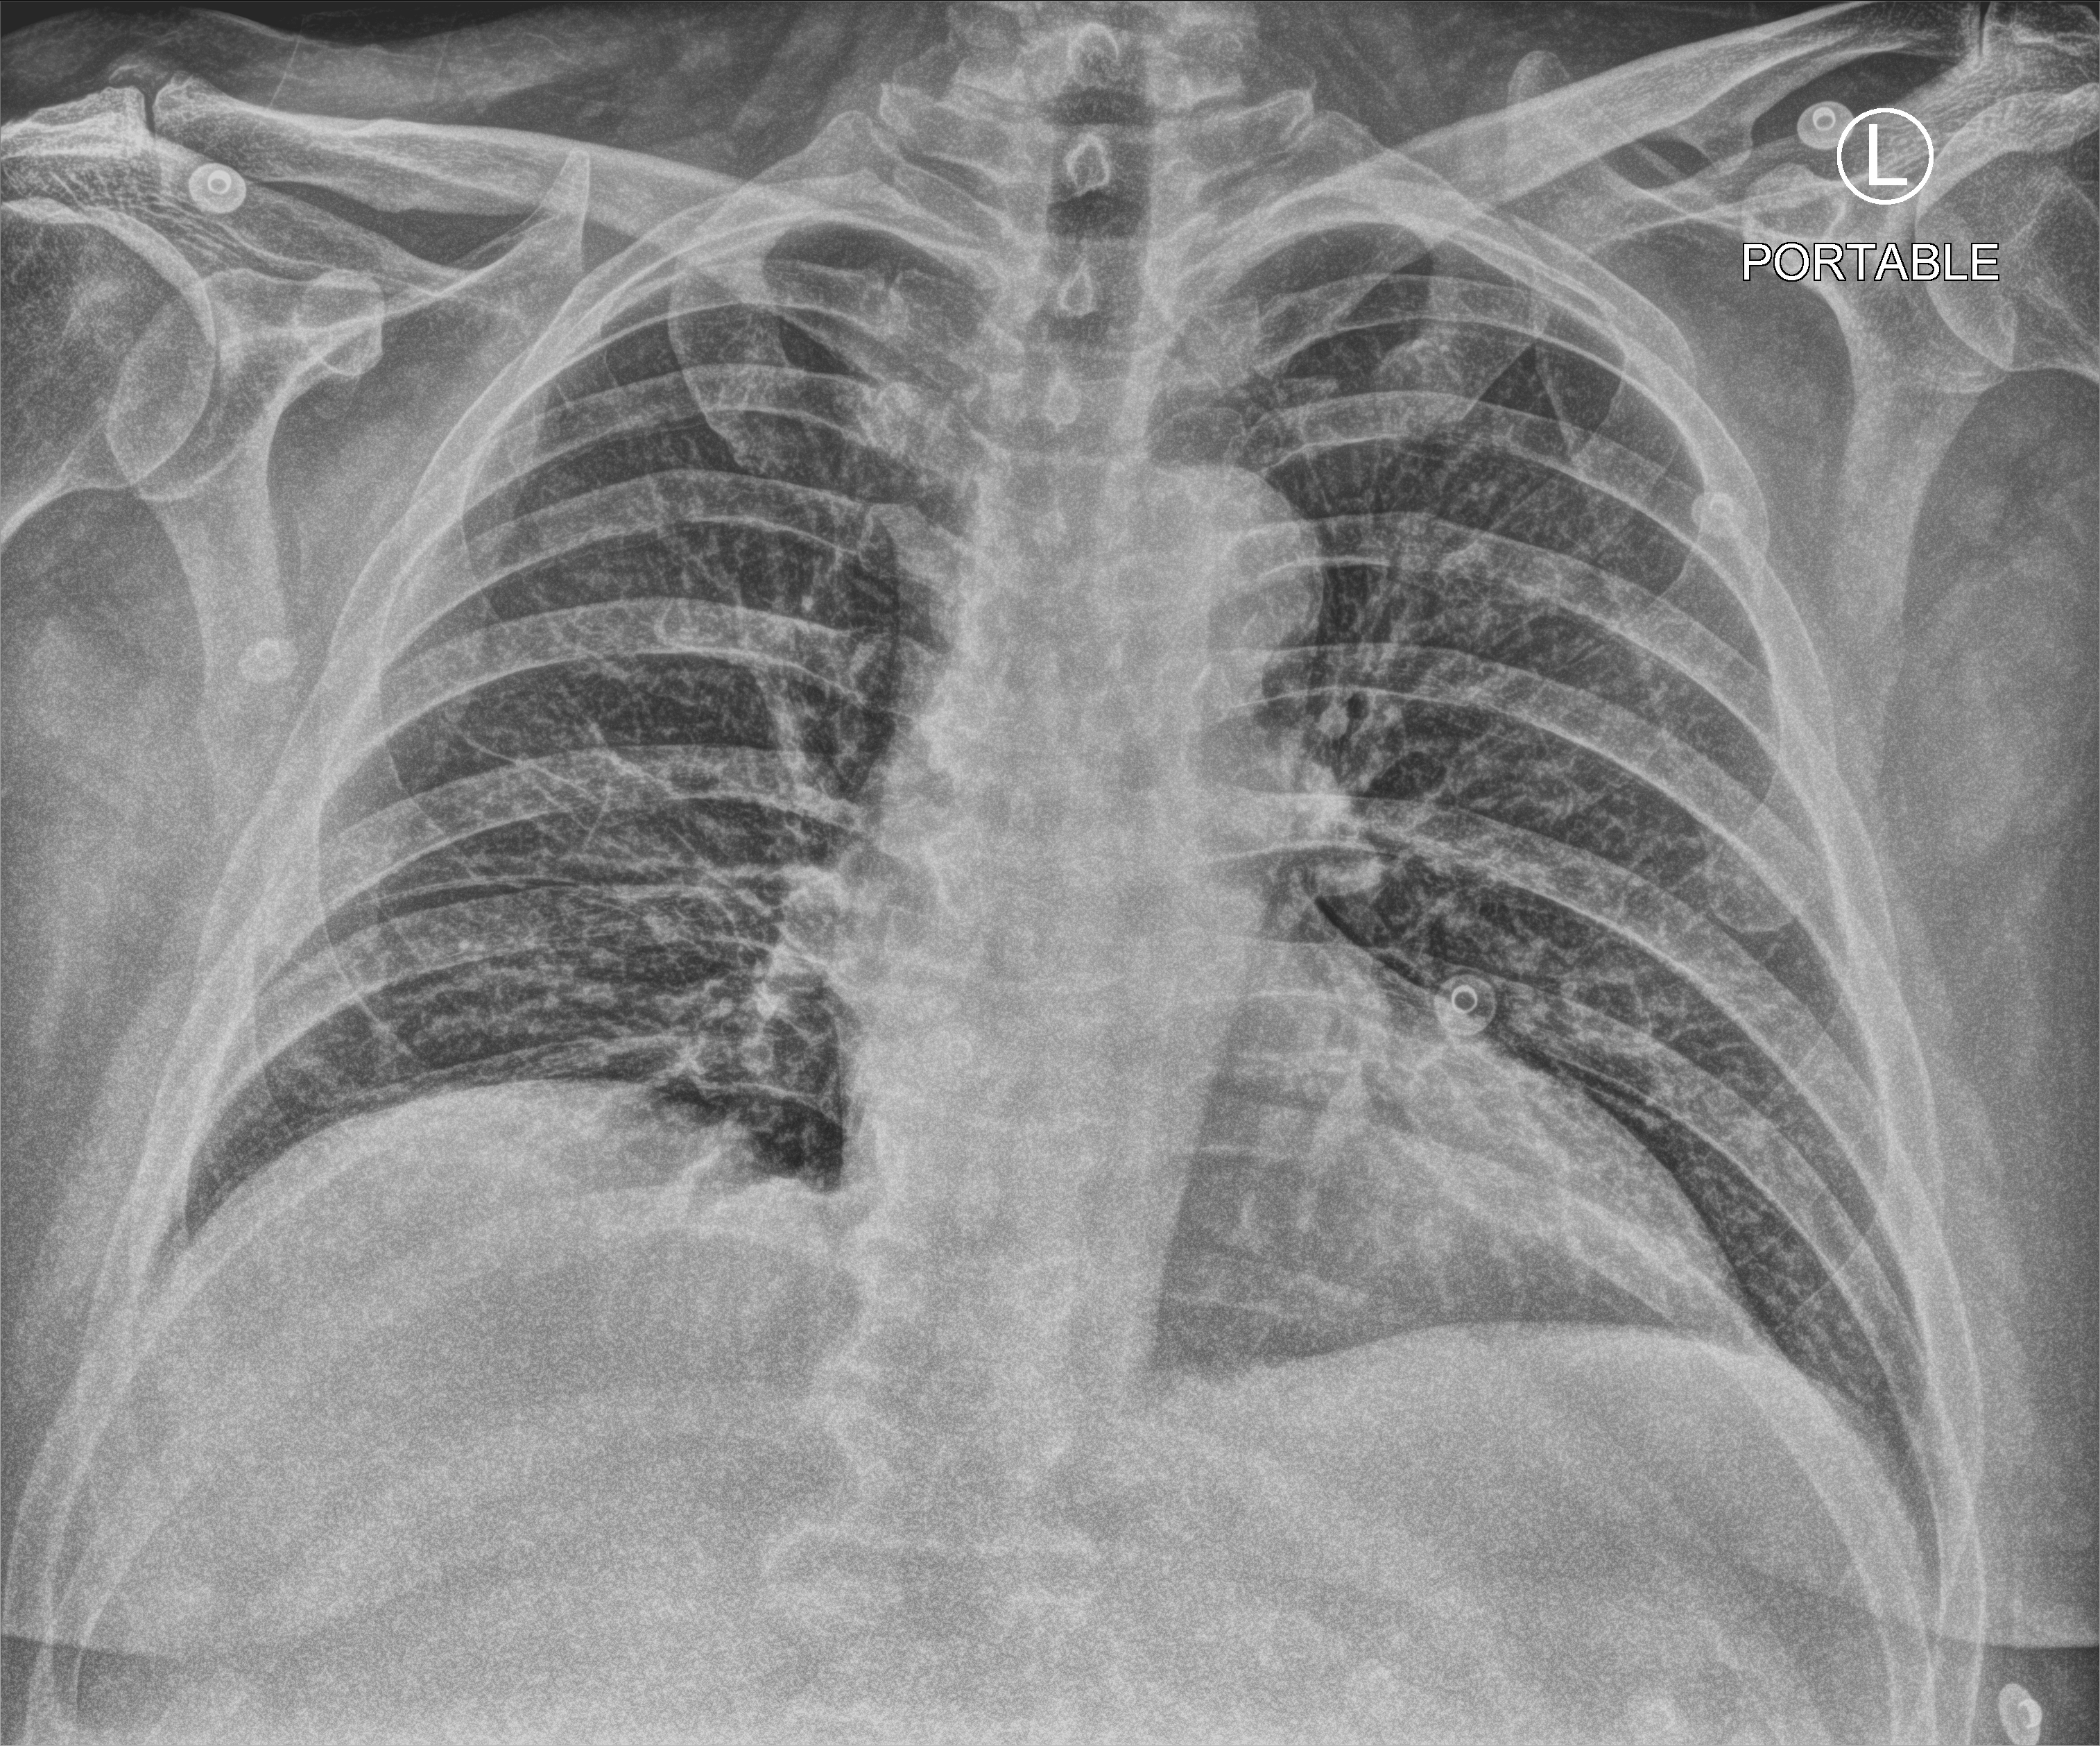
Bedside chest radiograph (computed radiography), anteroposterior (AP) projection. Patient hospitalised with COVID-19; male, aged 60–74 years.
Admission-level facts for this patient (not findings on this image; timing relative to this image not recorded): length of hospital stay: 5 days.